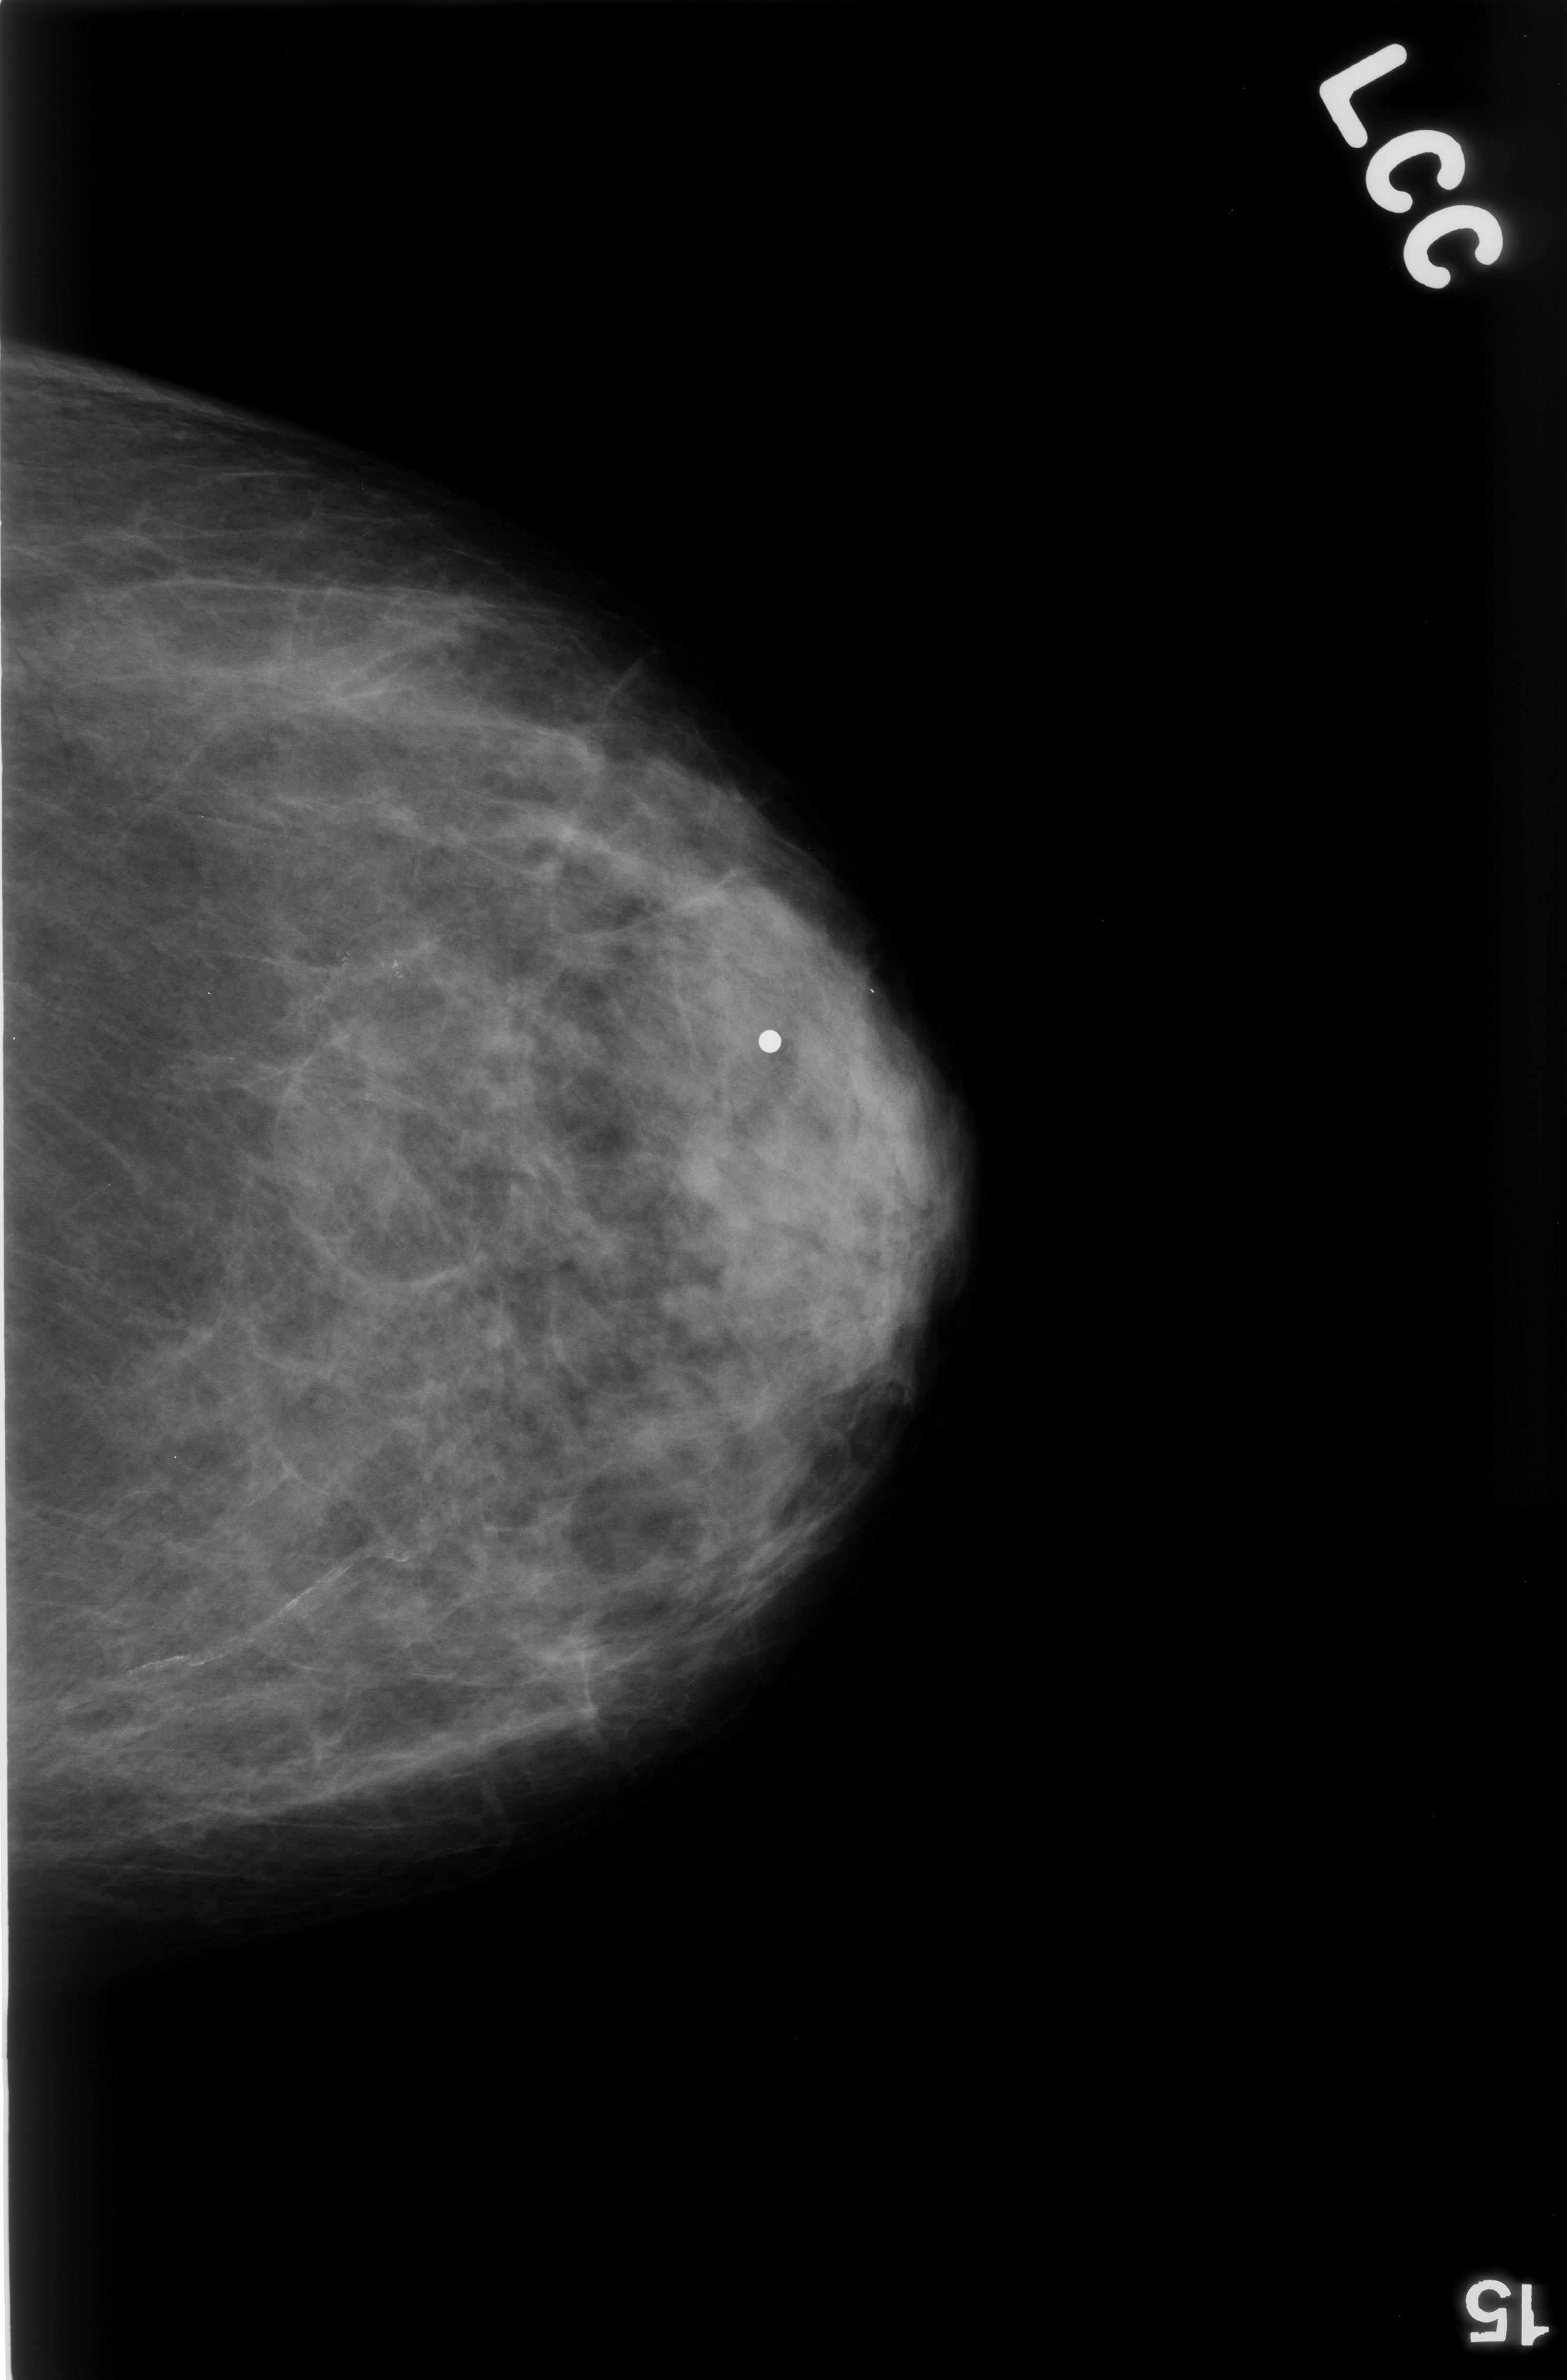
Scanned film-screen mammogram. Left breast. Craniocaudal (CC) view. BI-RADS breast density category 2 (scale 1–4). 1567 × 2380 image matrix.
Marked abnormalities (boxes around the expert regions of interest):
- calcifications, morphology pleomorphic, distribution clustered; BI-RADS assessment category 4; pathology (as recorded): benign: bounding box (x1, y1, x2, y2) in pixels: (315, 880, 498, 1033)